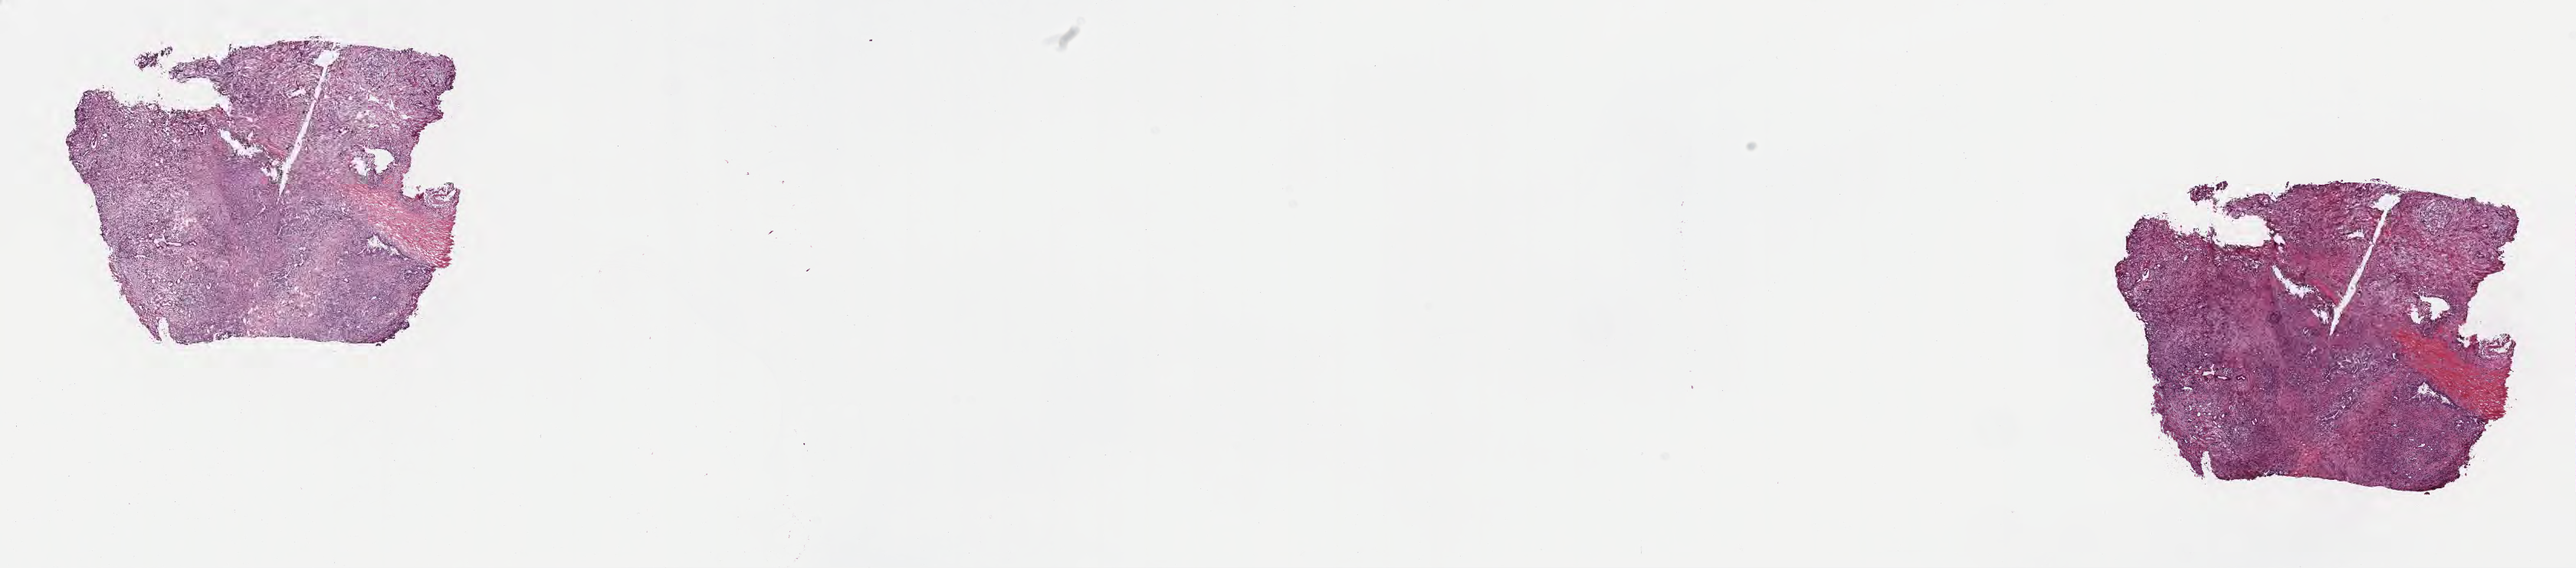
Hematoxylin and eosin (H&E) whole-slide image, low-resolution overview of the scanned area, about 27.2 x 6.0 mm, cryosection, primary tumor, site: tail of pancreas. Female, age 79 years at initial diagnosis. Pathologist review of this section (percent, as recorded): tumor cells 38%, tumor nuclei 50%, stromal cells 61%, necrosis 1%, normal cells 0%. Inflammatory infiltration, as recorded: lymphocyte infiltration 42%, monocyte infiltration 1%, neutrophil infiltration 0%.
Section: top of the tissue portion. Histologic diagnosis: Infiltrating duct carcinoma, NOS.